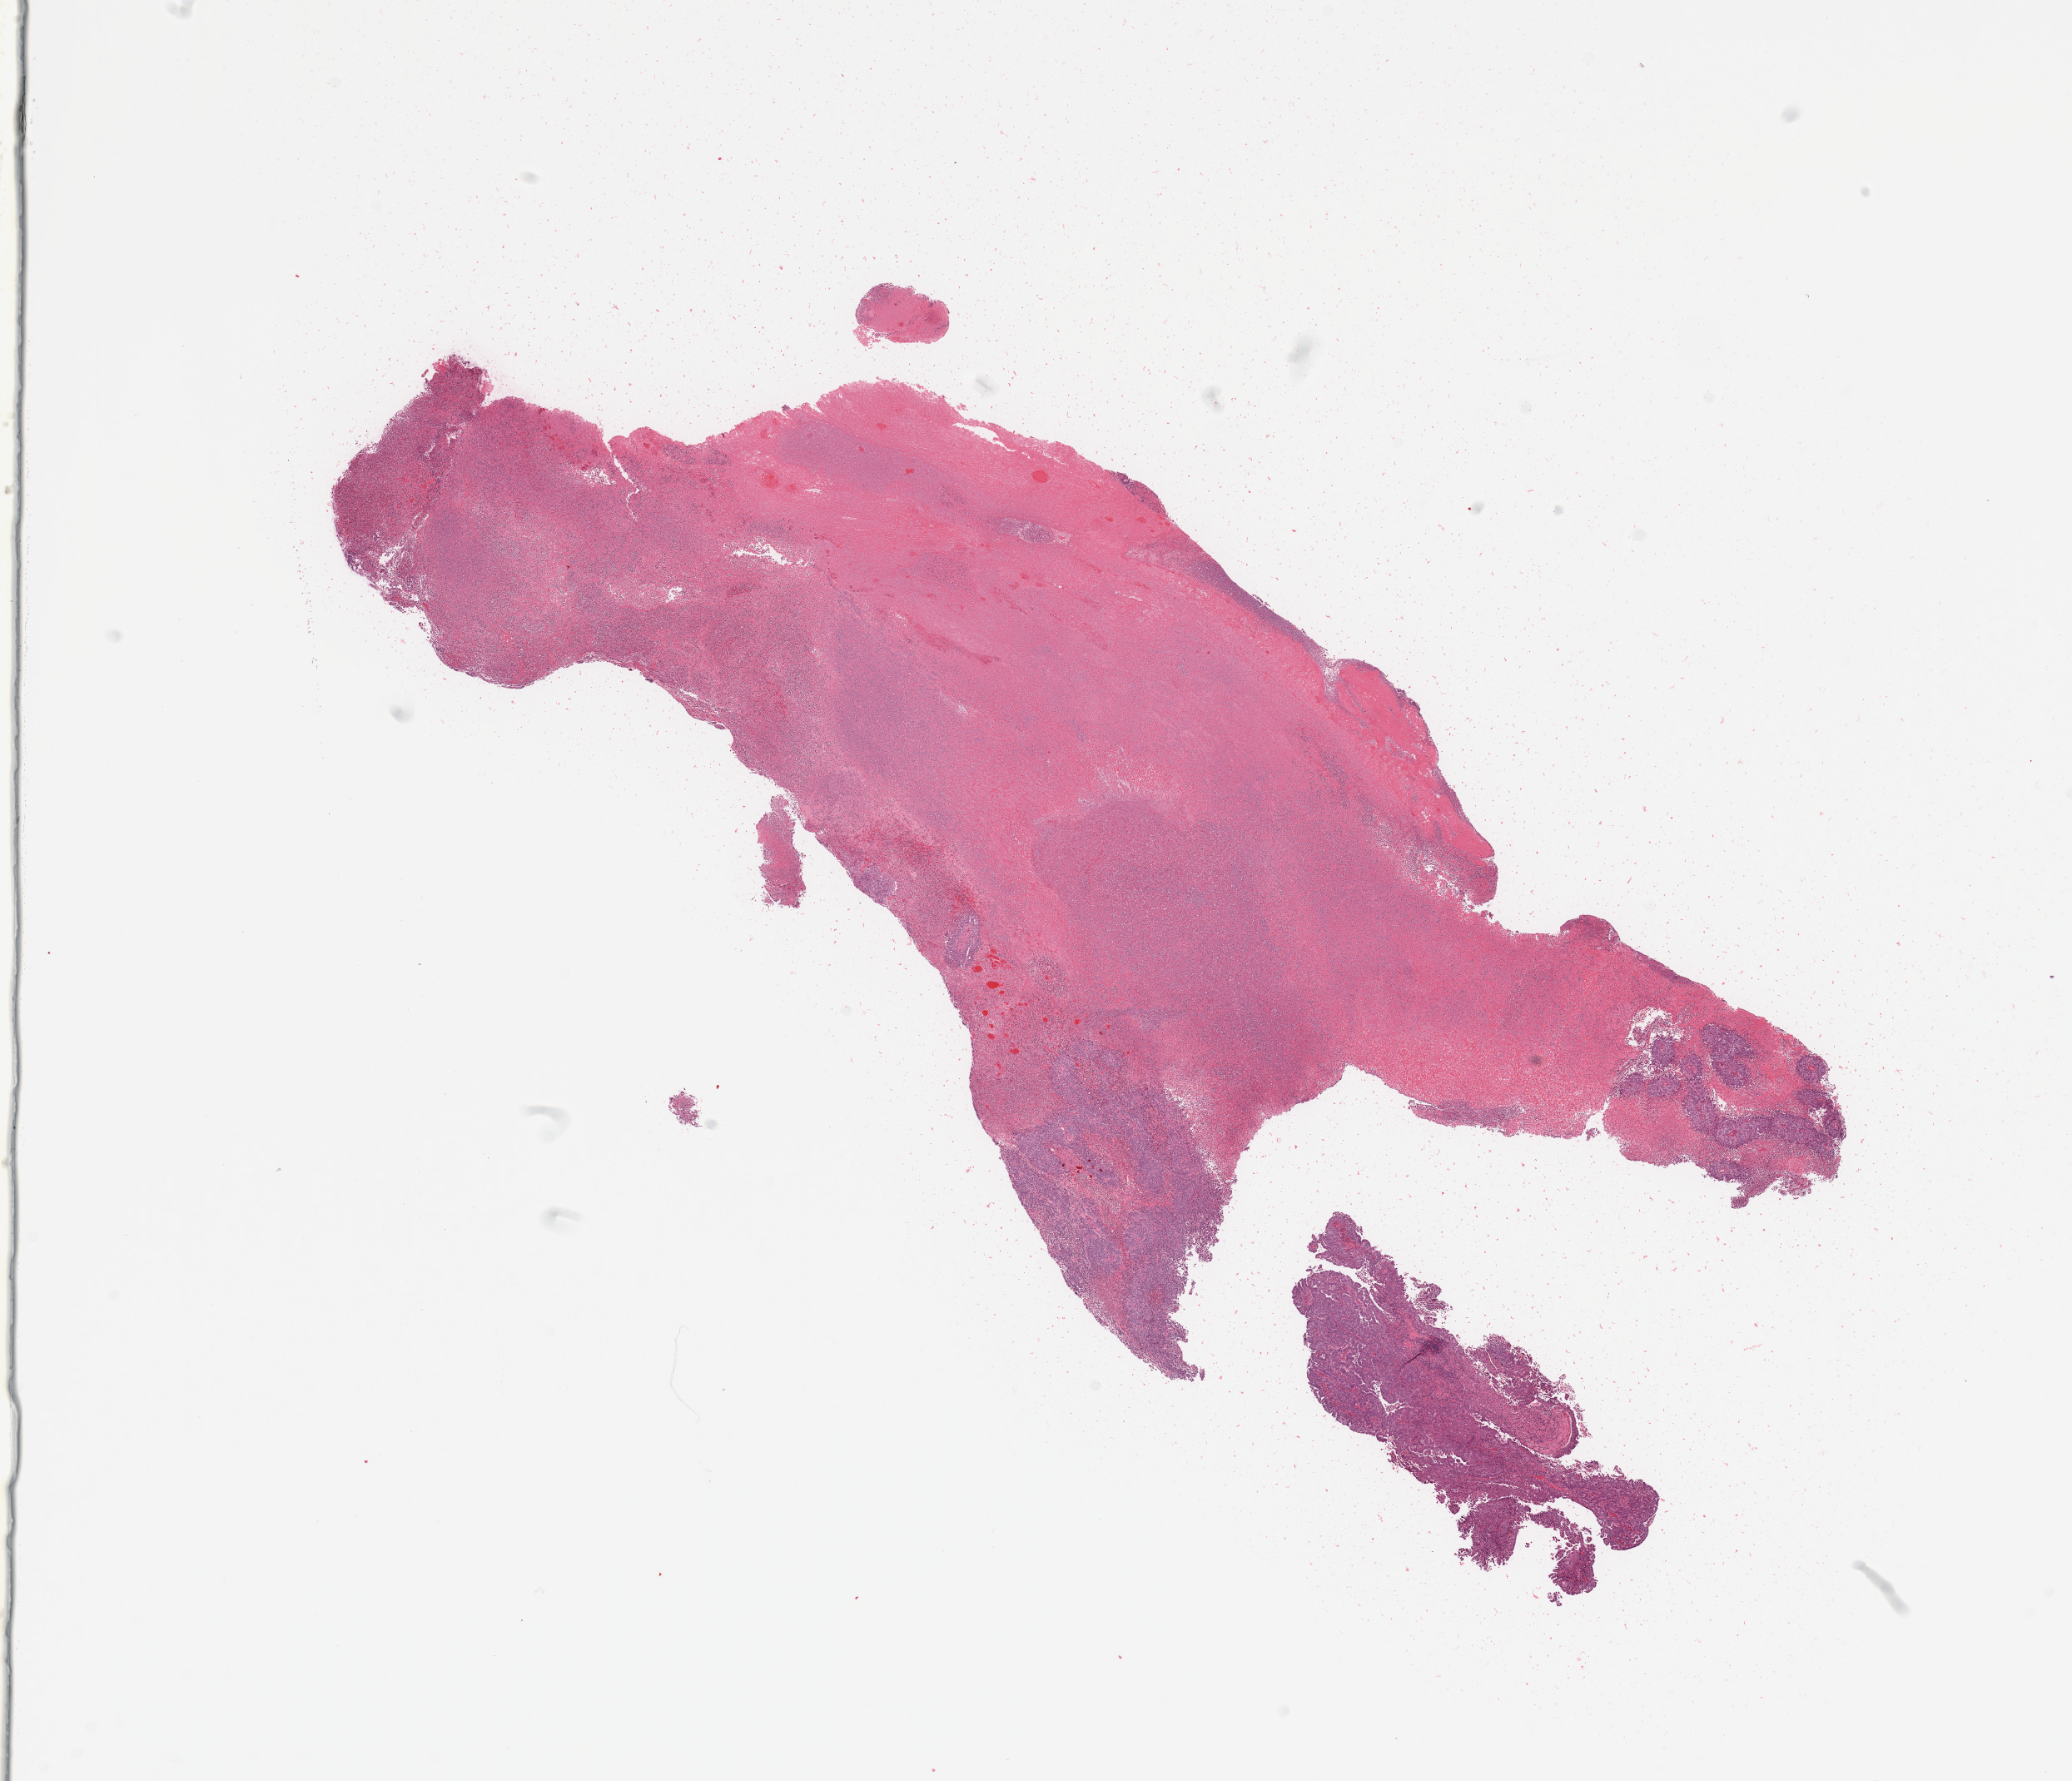
Hematoxylin and eosin (H&E) stained whole-slide image — shown as a low-resolution overview of the whole scanned area (about 19.7 x 16.9 mm), tumour tissue sample, uterus. Female, 51 y/o. Histologic grade: G3 (poorly differentiated).
Histologic diagnosis: Endometrioid adenocarcinoma, NOS.